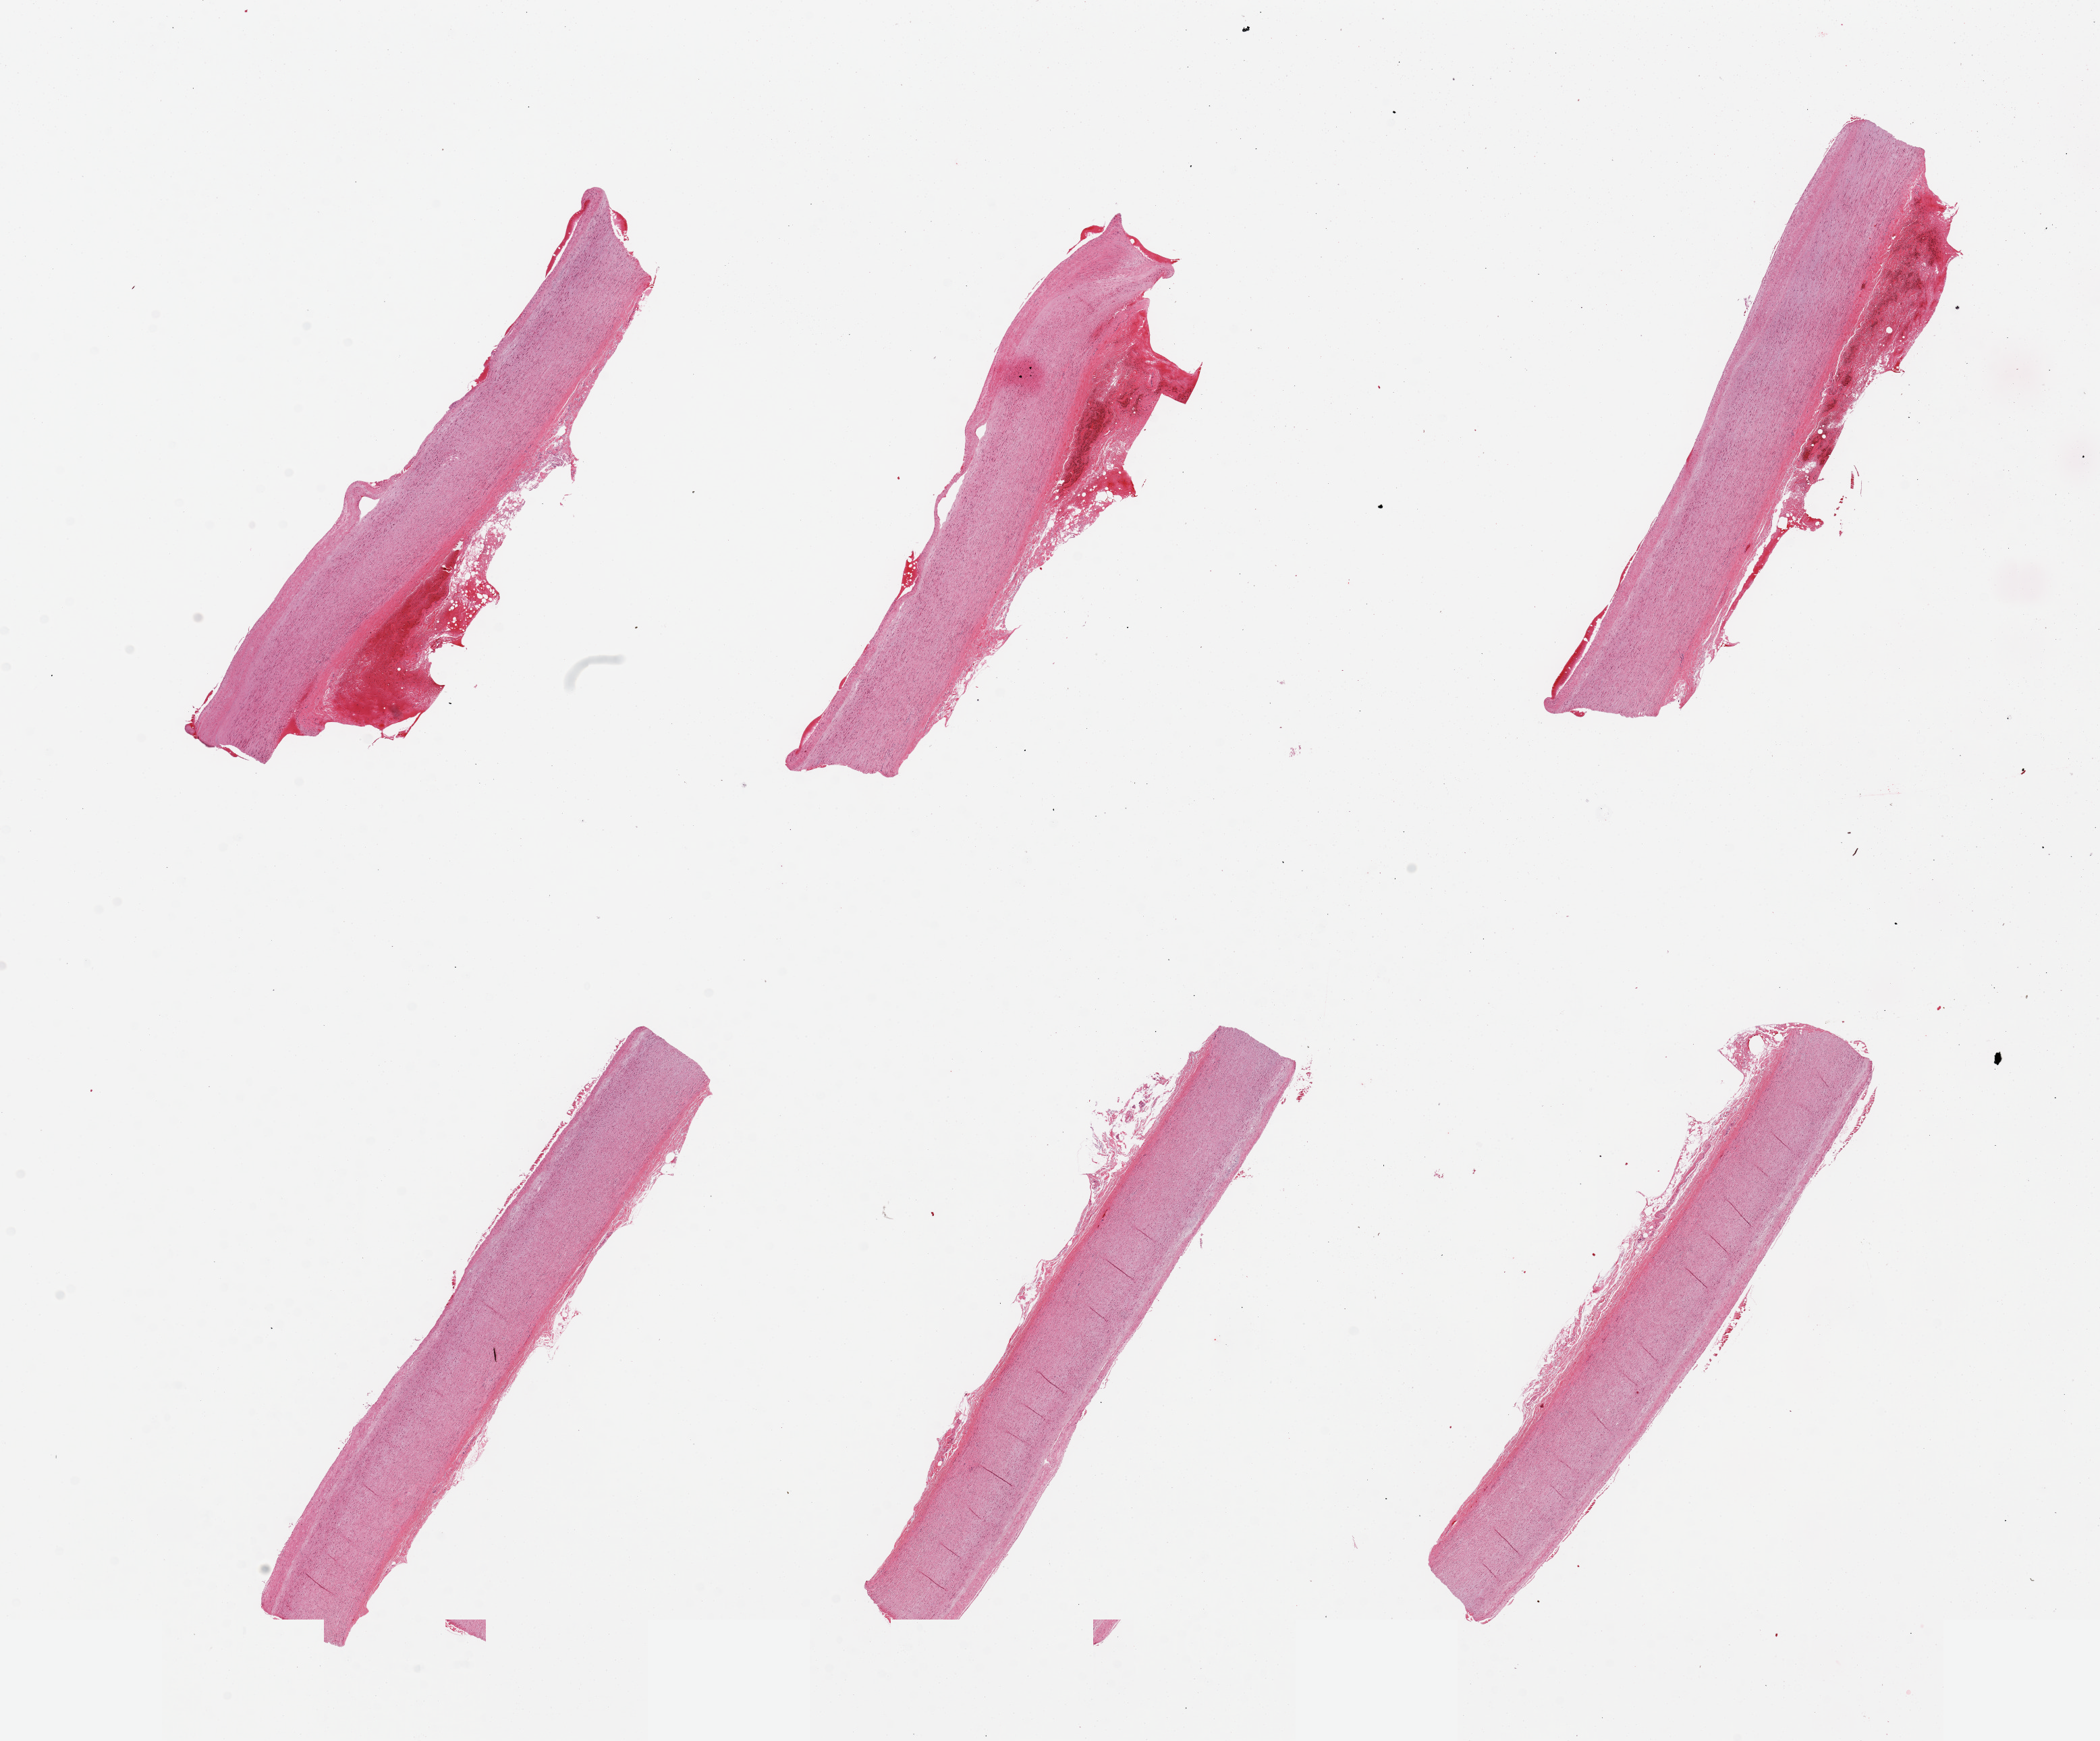
Whole-slide image, hematoxylin and eosin (H&E) stain, low-resolution overview of the scanned area, about 24.6 x 20.4 mm; PAXgene-fixed, paraffin-embedded tissue; sampled site (target tissue): aorta; tissue donor sample. Female donor.
- pathologist's review note for this sample: 6 pieces, mild atherosclerosis